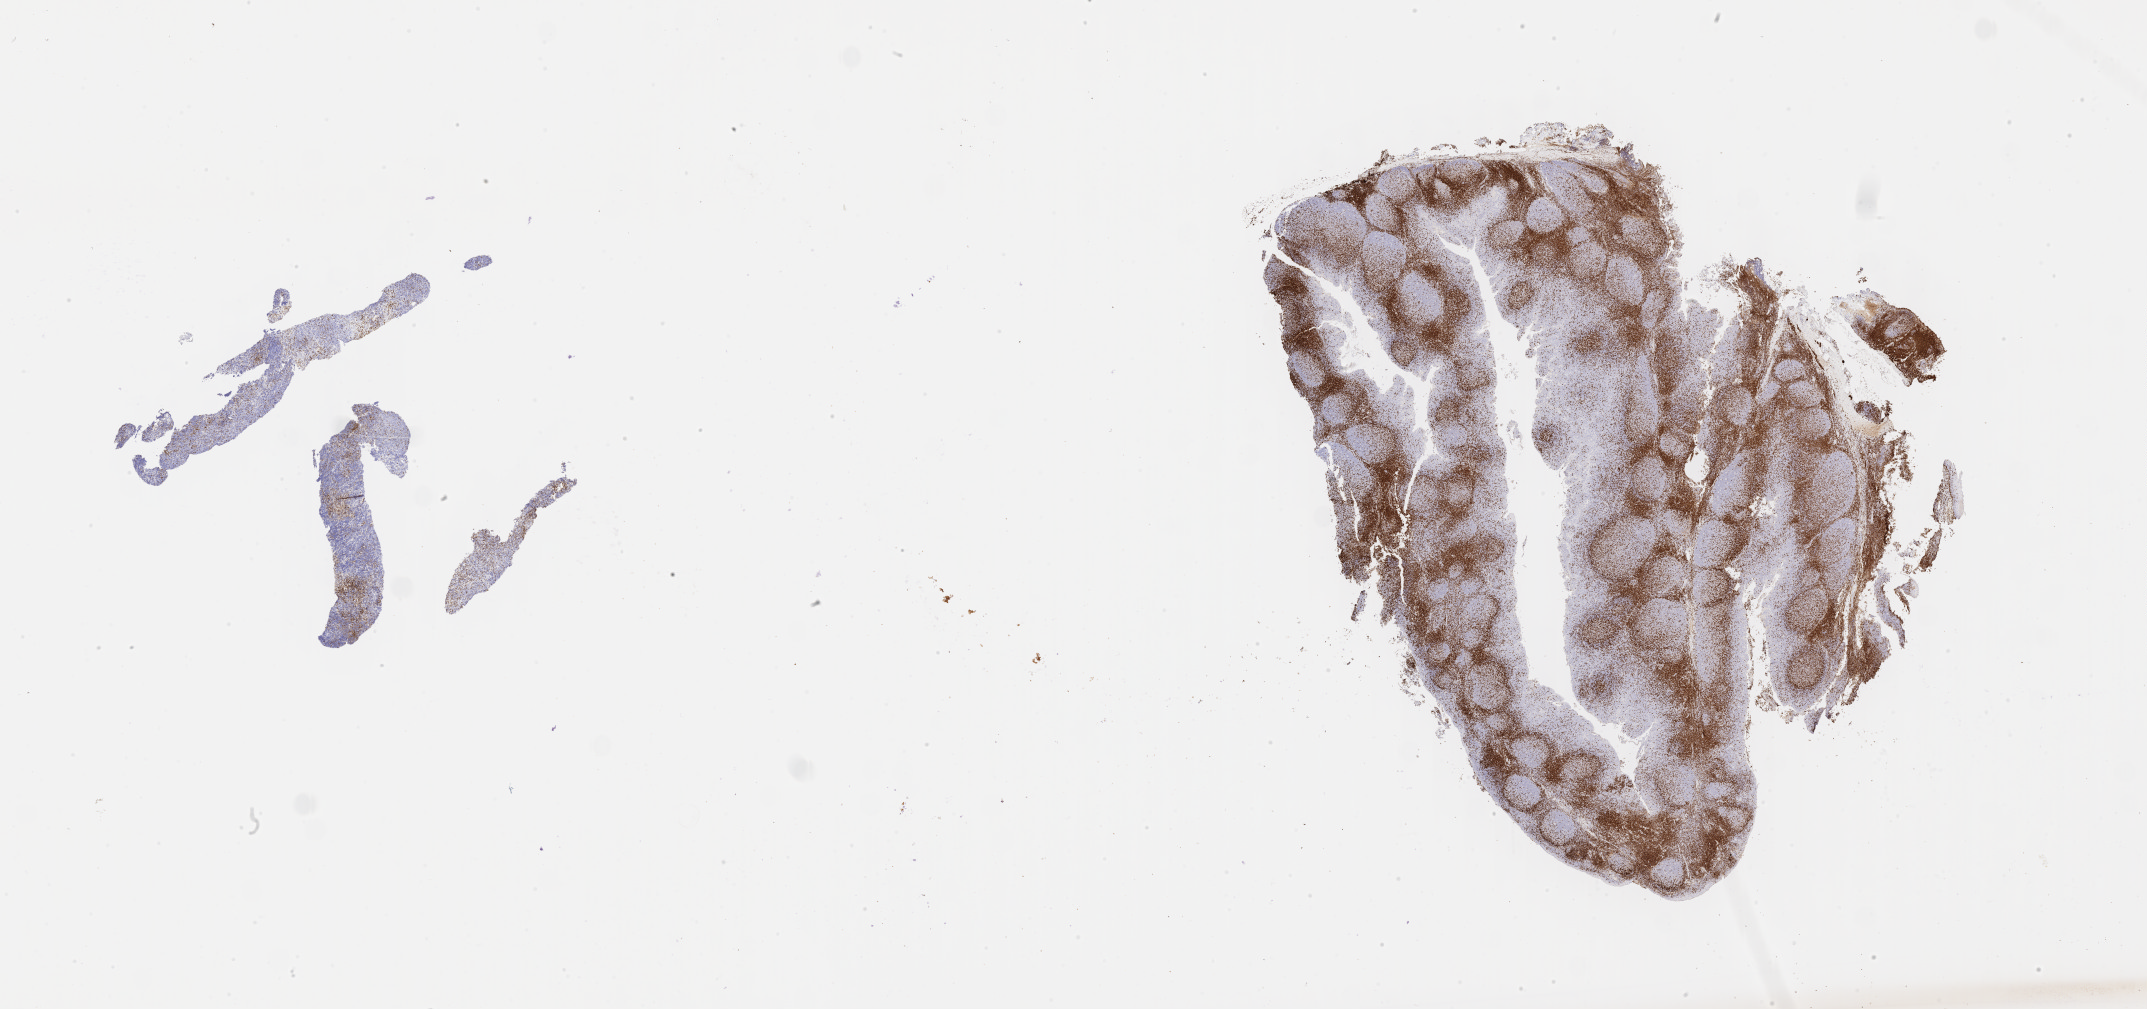
IHC for CD3, whole-slide image — shown as a low-resolution overview of the whole scanned area (about 34.7 x 16.3 mm), tumor tissue, anatomic site: abdomen proper. Patient: male, age at initial diagnosis 2 years.
Diagnosis: Diffuse large B-cell lymphoma, NOS.